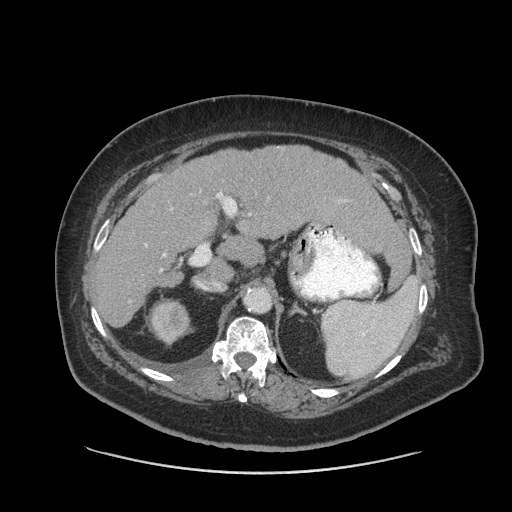
Contrast-enhanced abdominal CT (liver protocol), one axial slice; slice 51 of 91 in the series (ordered by position); reconstruction kernel STANDARD; 140 kVp; soft-tissue window (W 400 / L 40 HU); 2.5 mm slice thickness; 512 × 512 image matrix, field of view 420 × 420 mm. Case-level facts recorded for this patient, not image findings: diagnosis: hepatocellular carcinoma (patient treated with transarterial chemoembolisation; whether this scan precedes or follows treatment is not stated here); TNM stage (as recorded): Stage-I; Child-Pugh class: A.
Outlined on this slice (semi-automatic segmentation, software-assisted and operator-edited):
- liver parenchyma outside the tumour (the mass and vessels are separate outlines, so this box may not span the whole liver): box from (x=94, y=146) to (x=394, y=326) px
- liver vessels: (x=145, y=192)–(x=223, y=256)